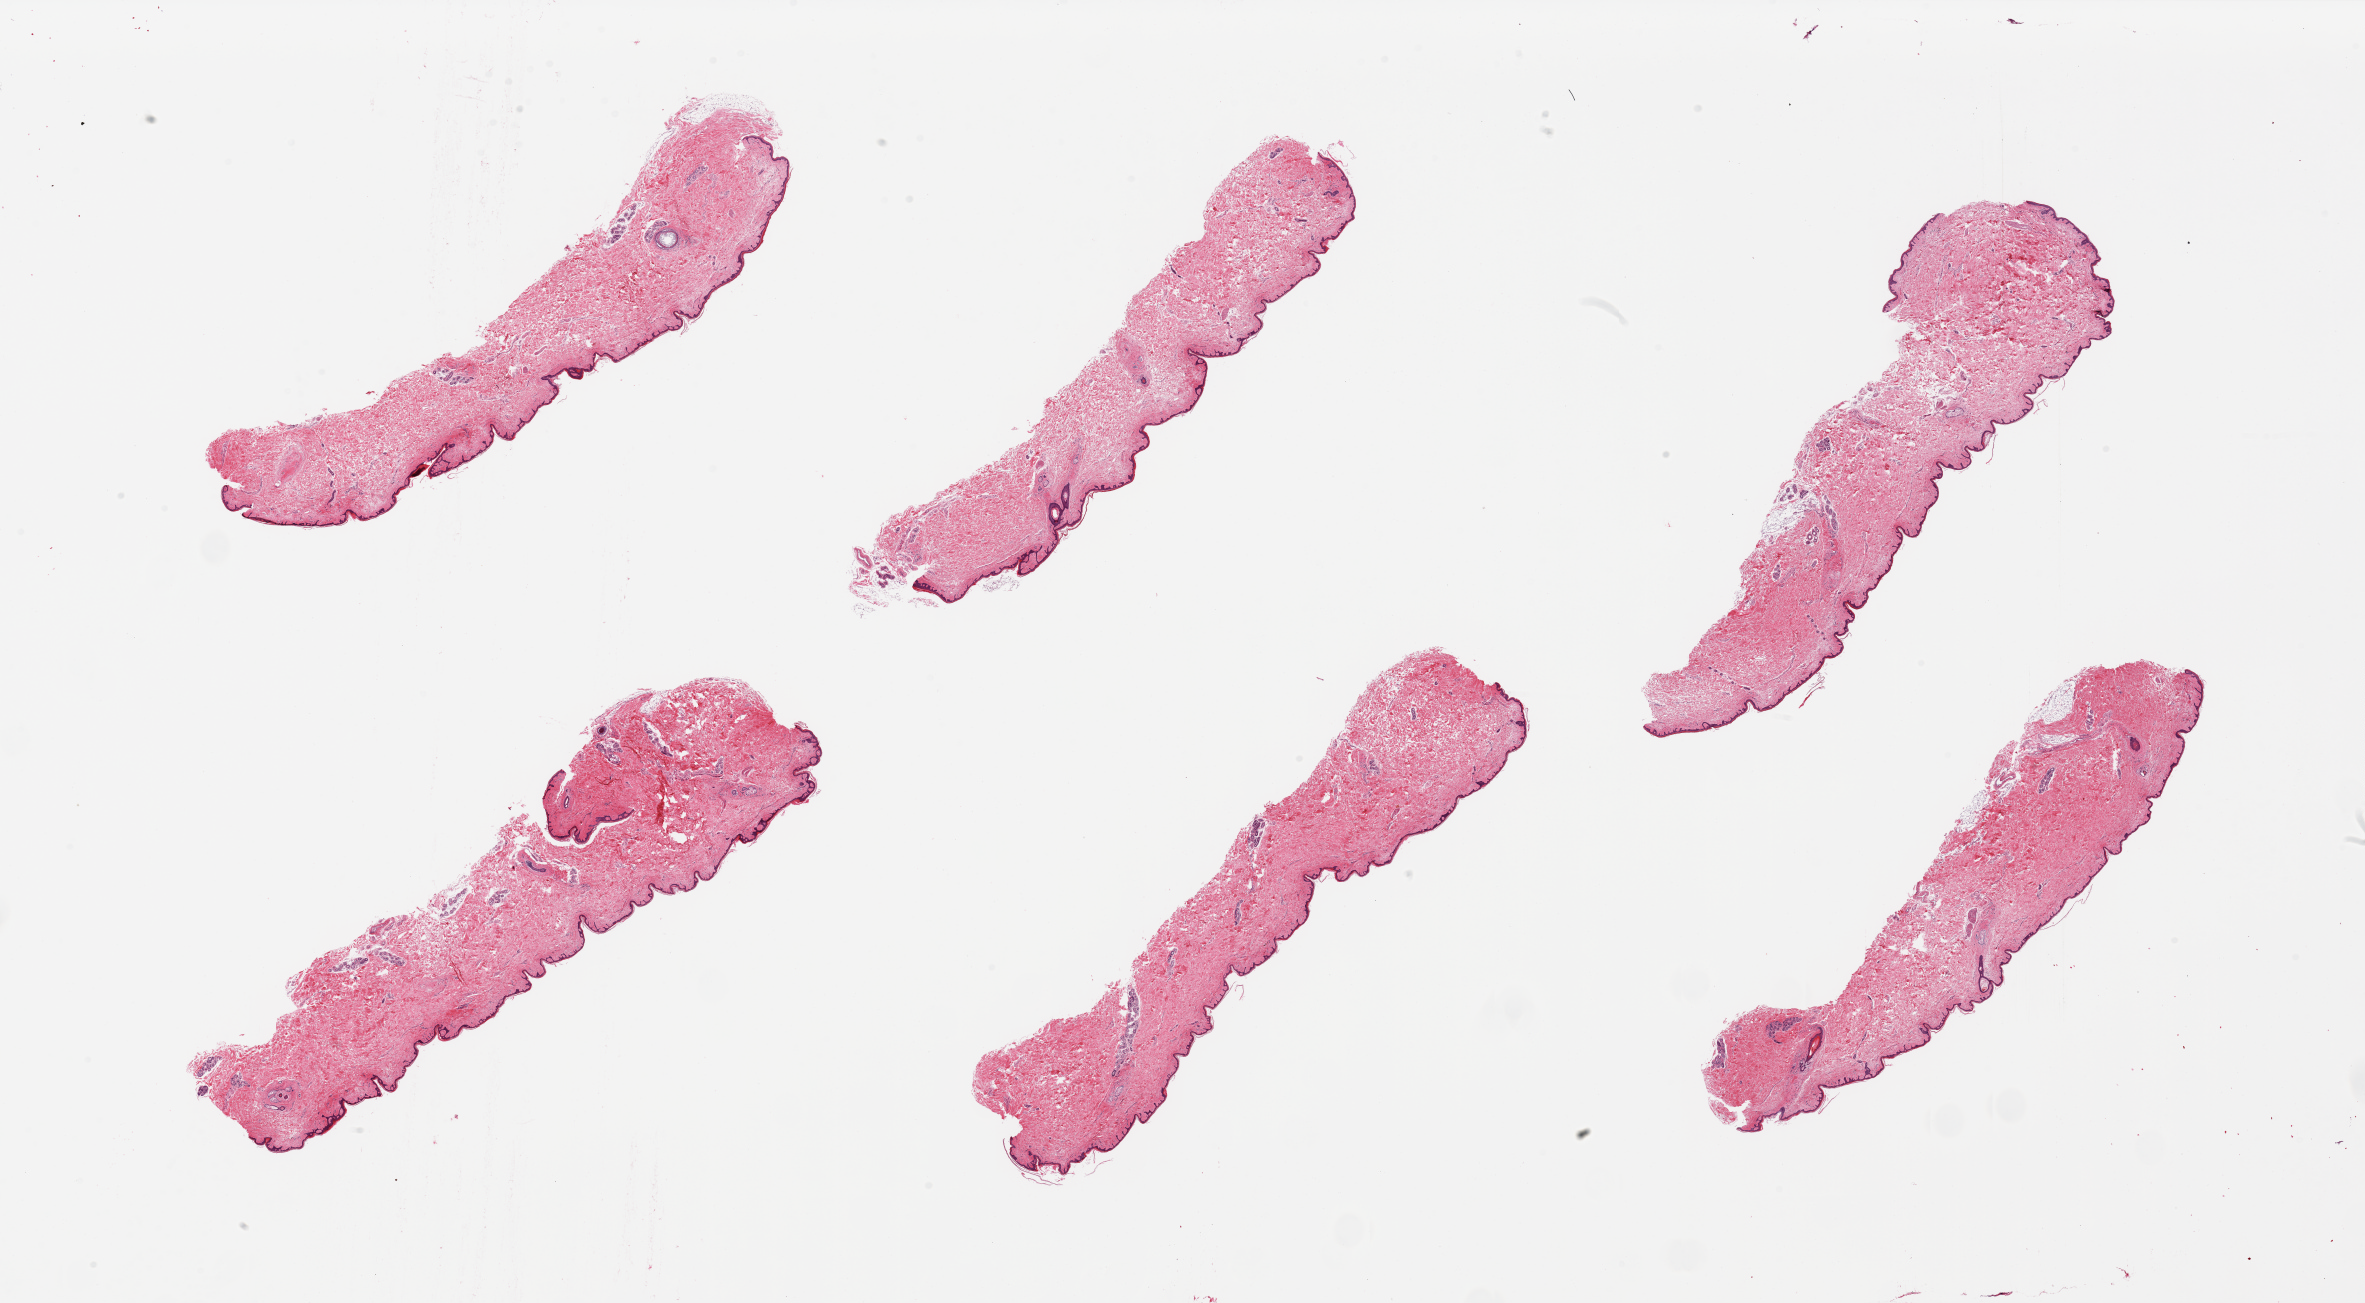
Digitized H&E-stained section — shown as a low-resolution overview of the whole scanned area (about 37.4 x 20.6 mm), PAXgene-fixed, paraffin-embedded tissue, section of skin of suprapubic region (target tissue), tissue donor sample.
- reviewer comment on this tissue sample: 6 pieces, minimal fat, sqamous epithelium is atrohpic, ~20-30 microns